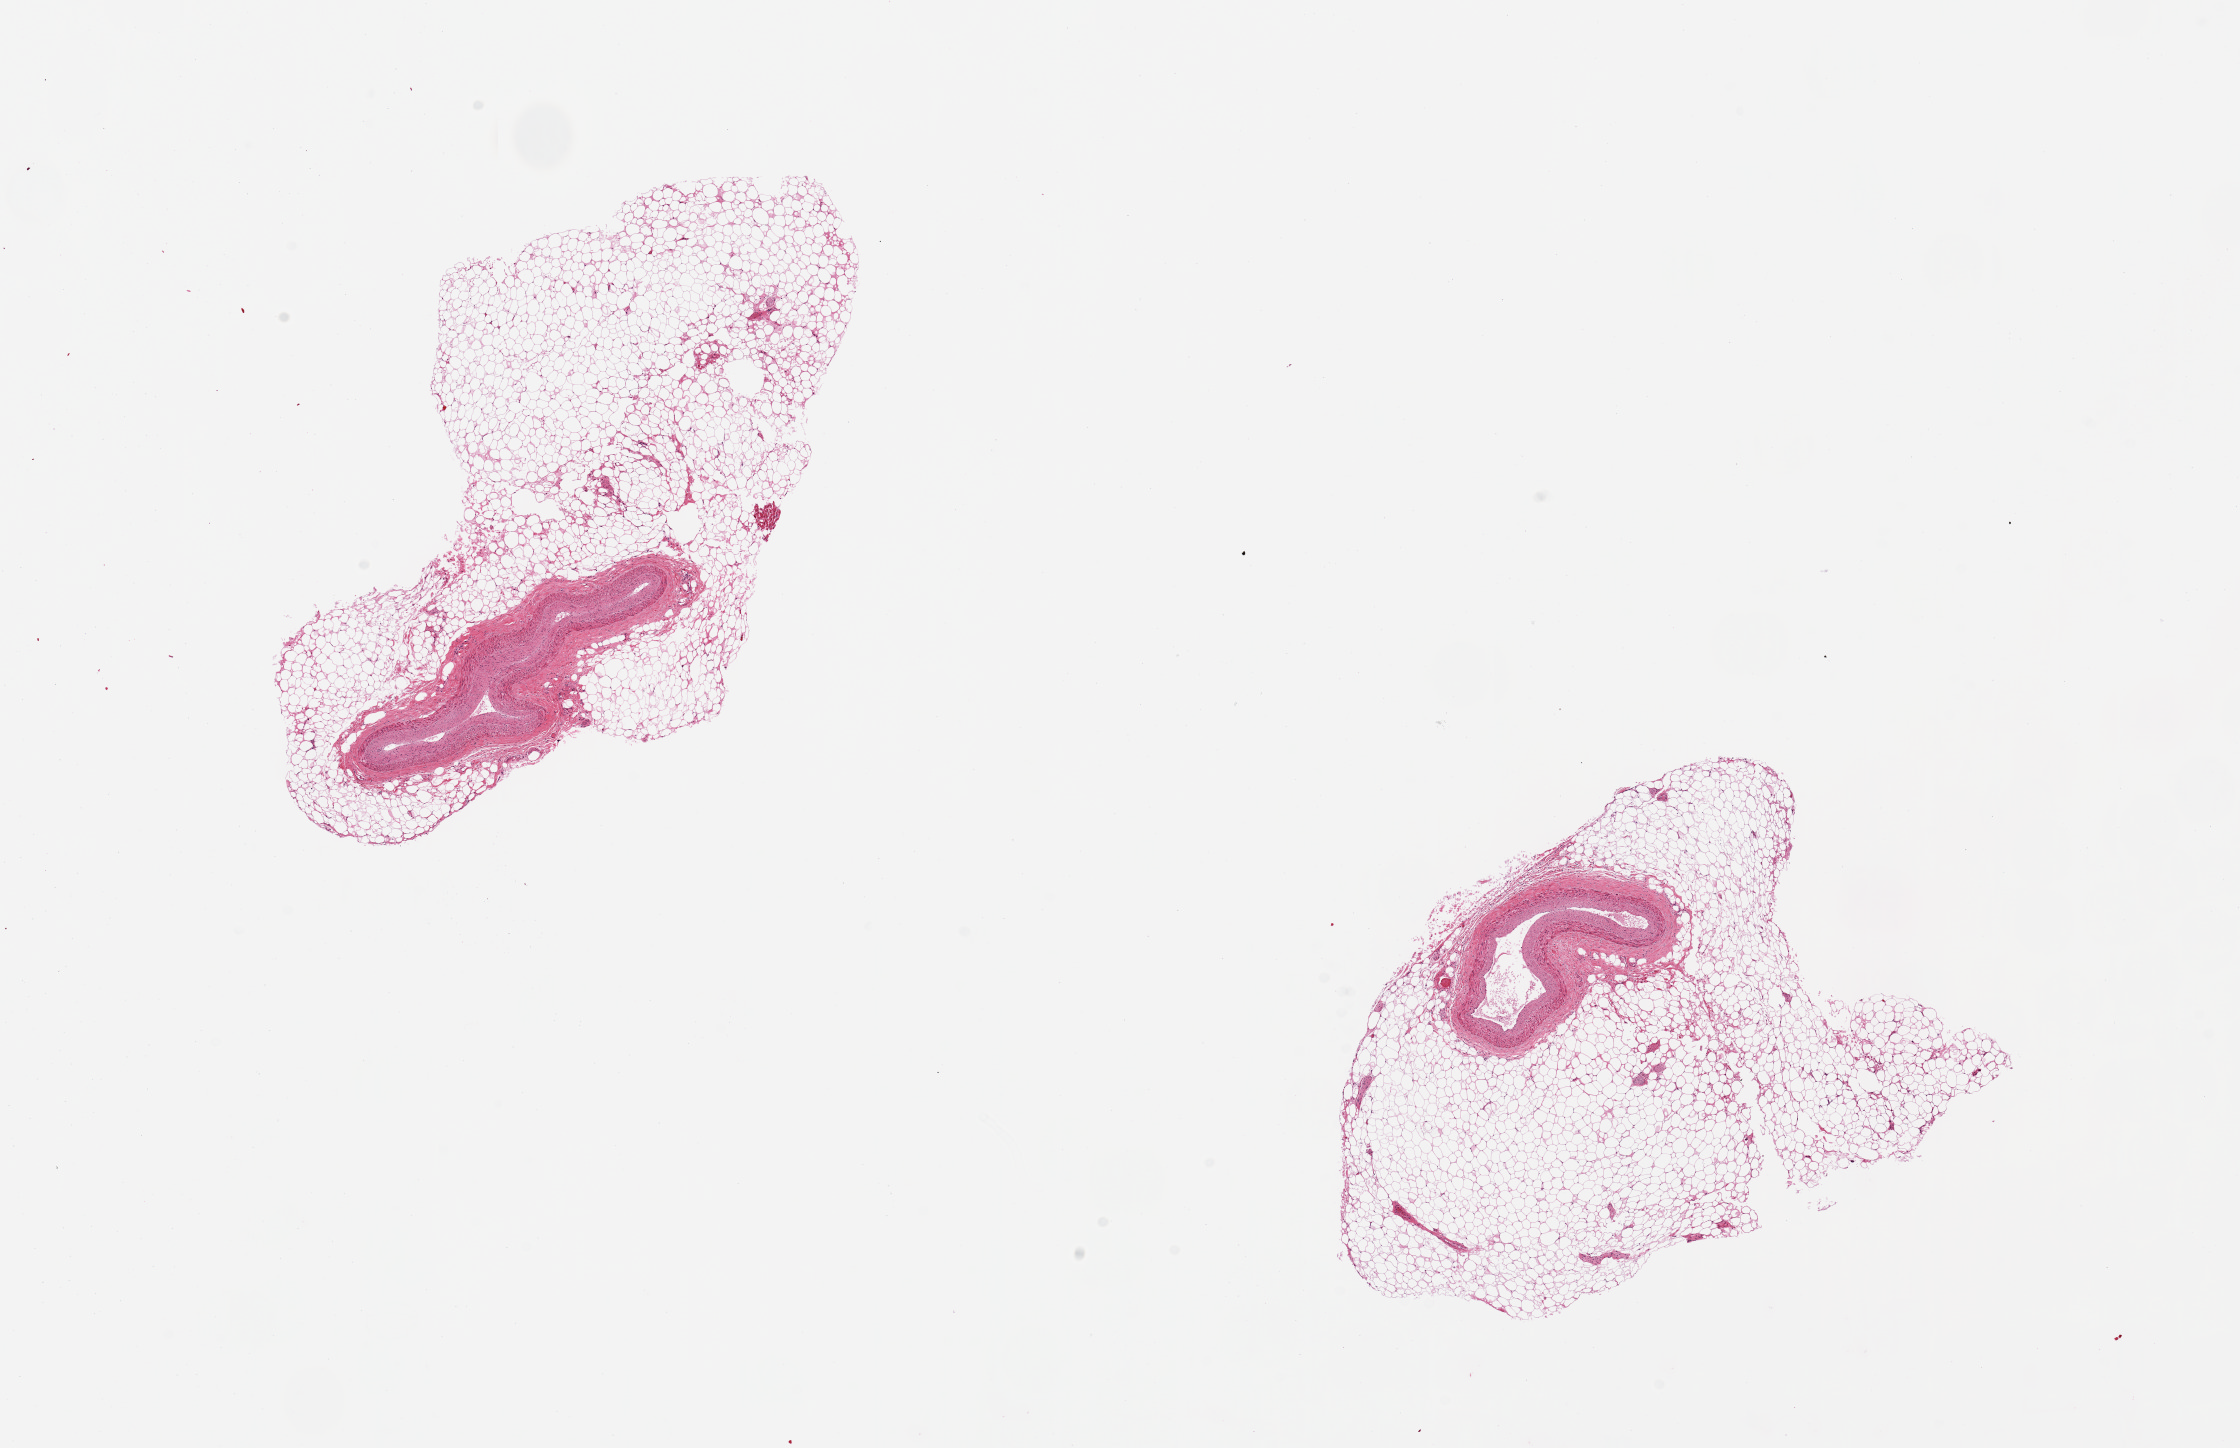
Haematoxylin and eosin whole-slide image, a low-resolution overview of the entire scanned area, about 17.7 x 11.5 mm, PAXgene-fixed paraffin-embedded (PFPE) section, sampled site (target tissue): coronary artery, tissue donor sample.
Reviewer comment on this tissue sample: 2 pieces 5 mm & 6 mm in greatest dimension. Moderate fibrous intimal sclerosis. ~80% of aliquot is adipose tissue.